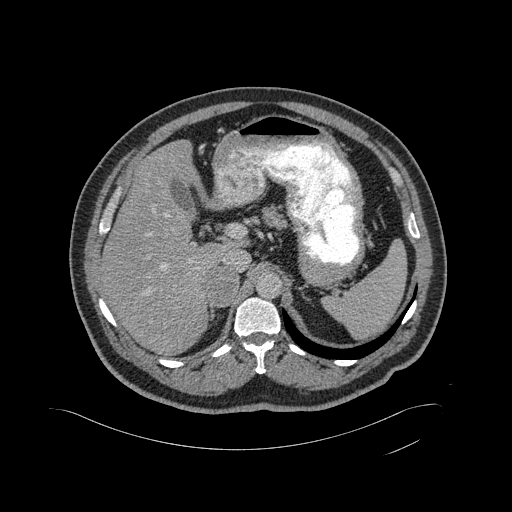
Contrast-enhanced abdominal CT, one axial slice; slice 328 of 433 in the series (ordered by position); intravenous contrast given; soft-tissue window (W 400 / L 40 HU); 2 mm slice thickness; 512 × 512 image matrix, field of view 500 × 500 mm. Male patient, age 56 years. Case-level facts recorded for this patient, not image findings: diagnosis: adrenocortical carcinoma; tumour side: right adrenal; tumour size at pathology: 11.6 cm; Ki-67 index: 50 %; stage (as recorded): 3.
Structures marked on this image (semi-automatic segmentation, software-assisted and operator-edited):
- mass: bounding box [x1, y1, x2, y2] px = [209, 266, 237, 305]